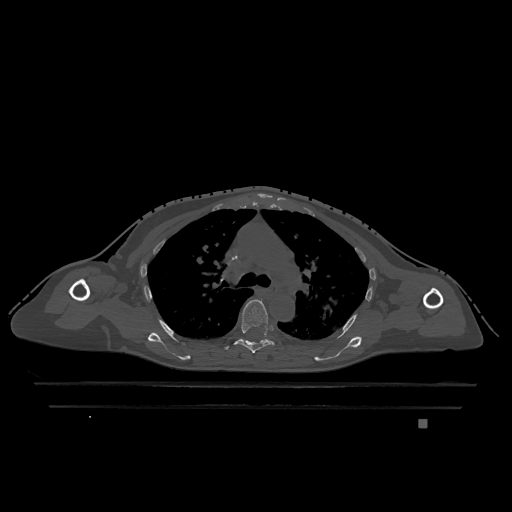
CT including the spine, one axial slice; slice 837 of 1317 in the series (ordered by position); bone window (W 1800 / L 400 HU); 512 × 512 image matrix, field of view 500 × 500 mm. Female patient, age 74 years. Case-level facts recorded for this patient, not image findings: primary cancer: lung; vertebrae with lytic lesions (as recorded): T1, T4, T5, T6, L4, L5.
Outlined on this slice (semi-automatically segmented with operator editing):
- T5 vertebra: bounding box [x1, y1, x2, y2] px = [225, 299, 274, 353]